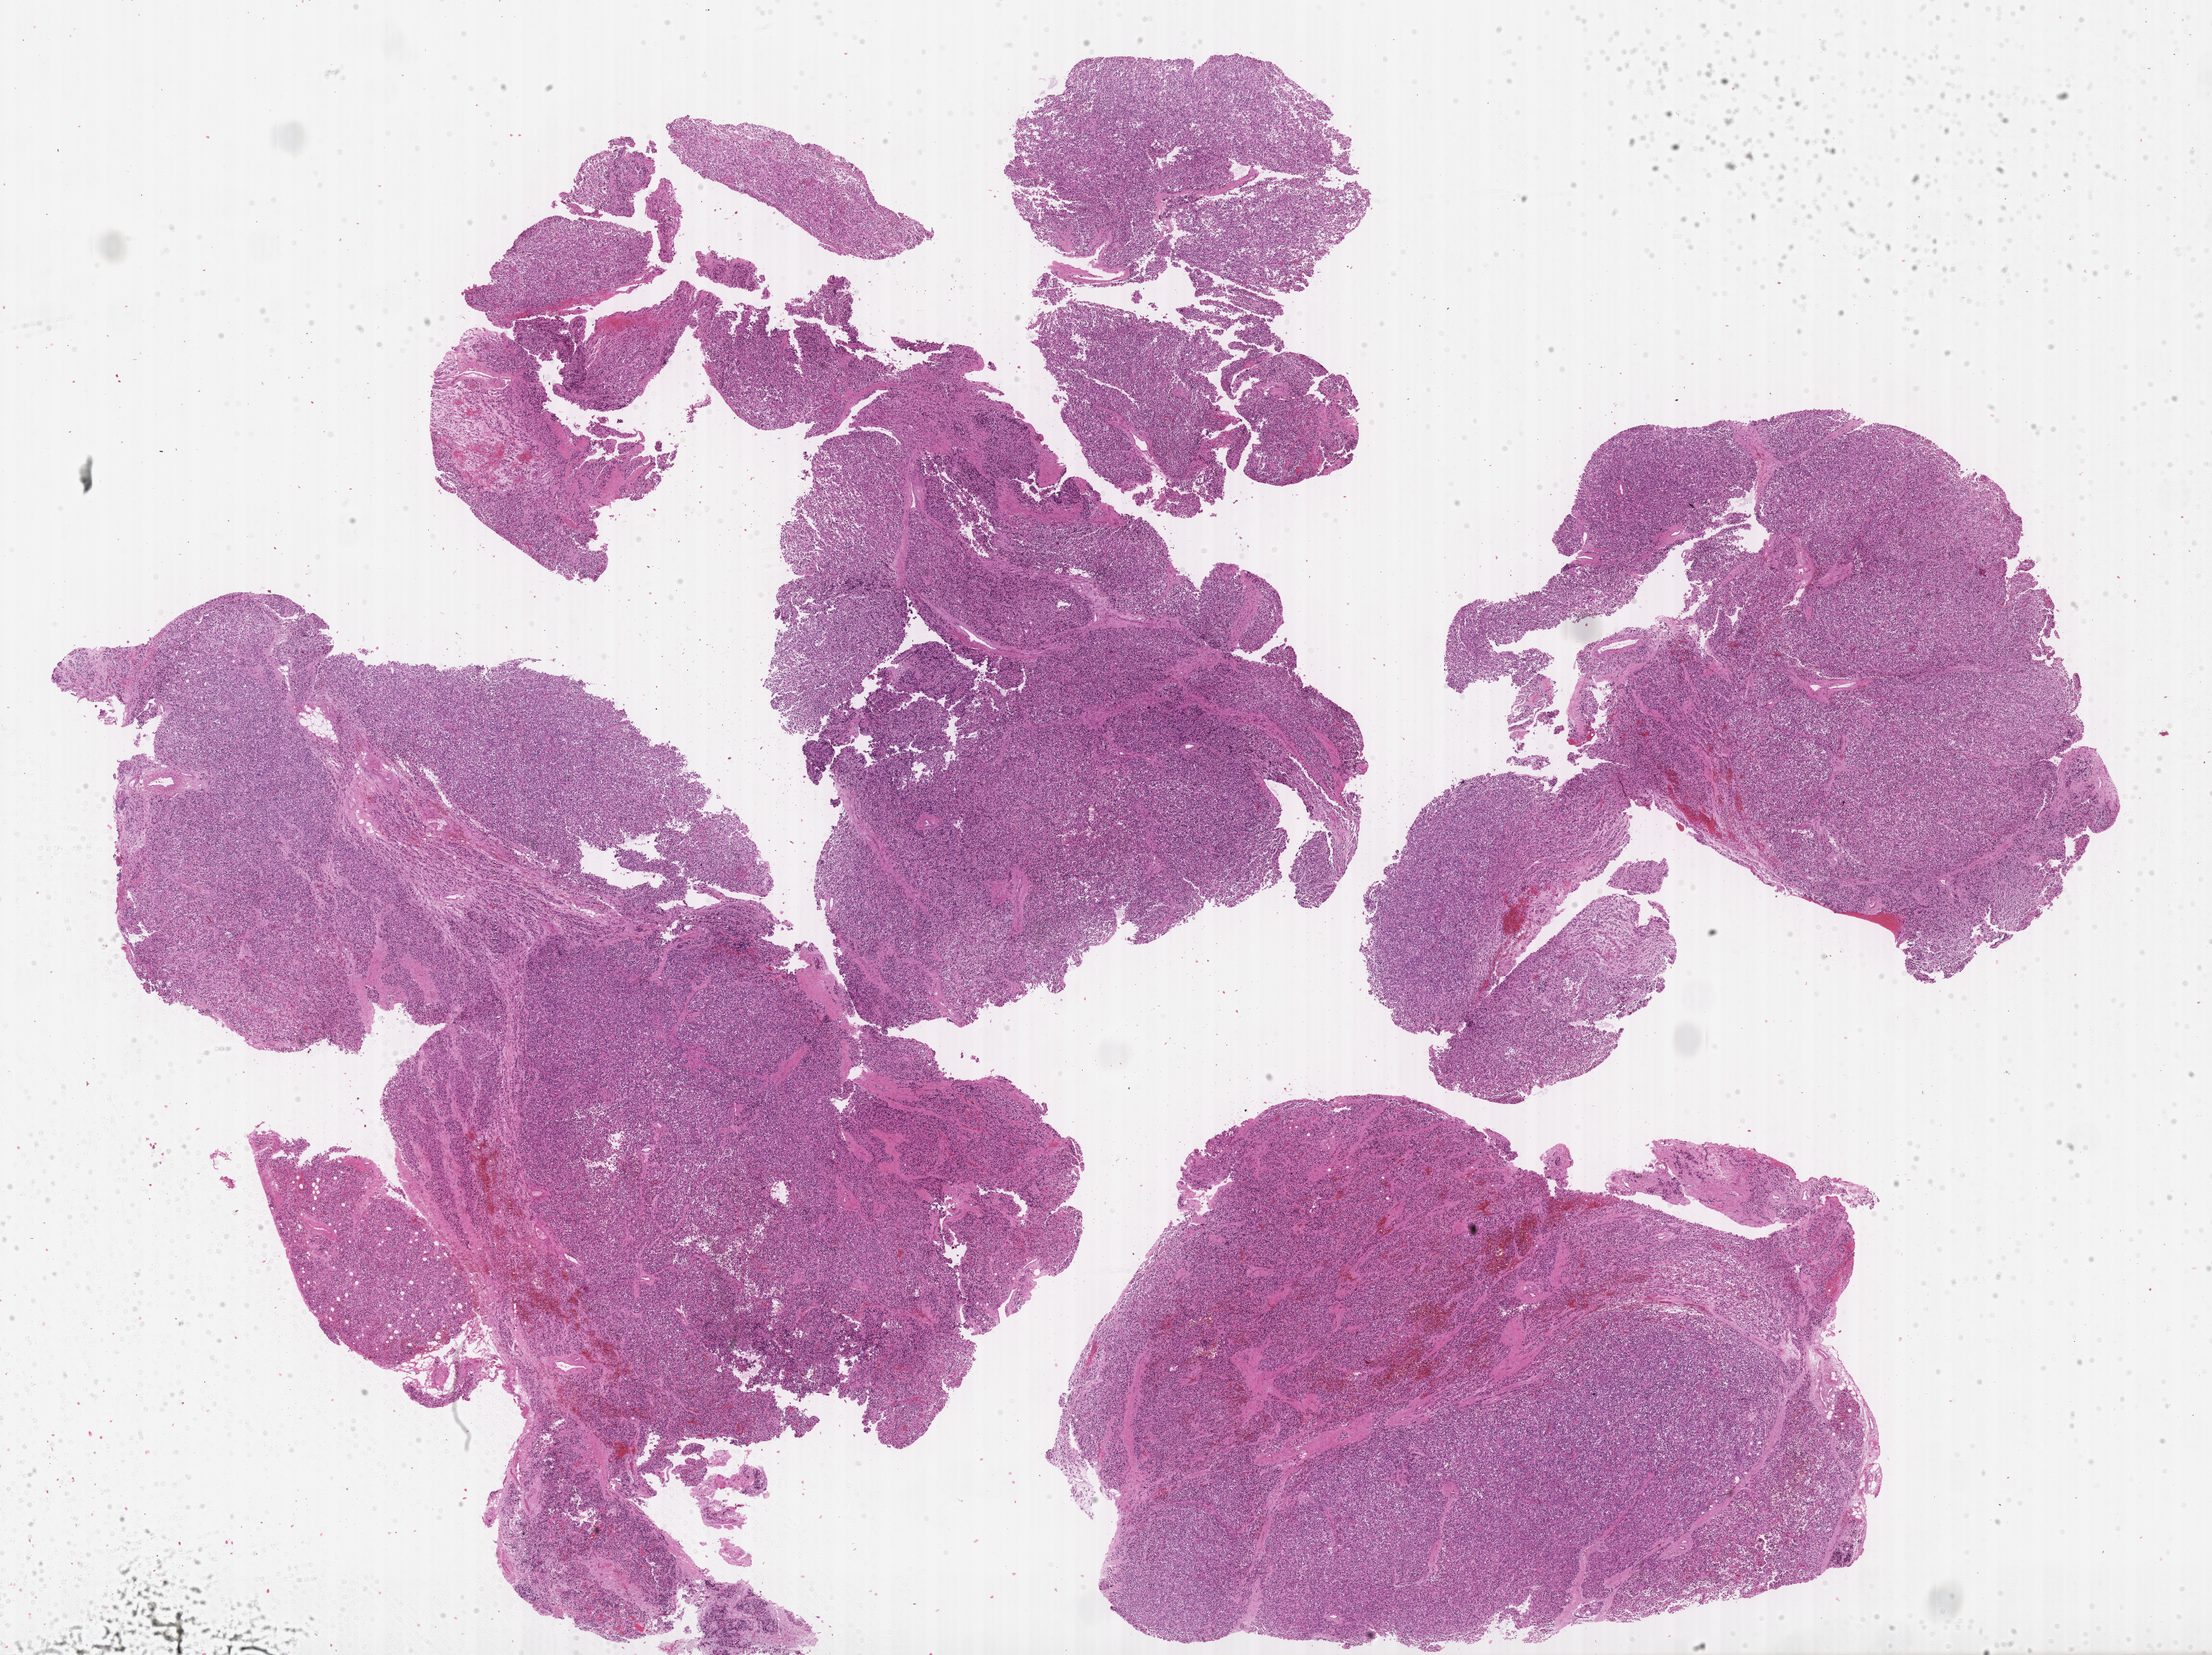
Hematoxylin and eosin (H&E) whole-slide image of tumor tissue — shown as a low-resolution overview of the whole scanned area (about 24.2 x 18.1 mm). Formalin-fixed, paraffin-embedded (FFPE) tissue. Site: eye, orbit-right. Male patient, age at diagnosis 11.2 years.
Diagnosis: rhabdomyosarcoma; histological classification: embryonal rhabdomyosarcoma.